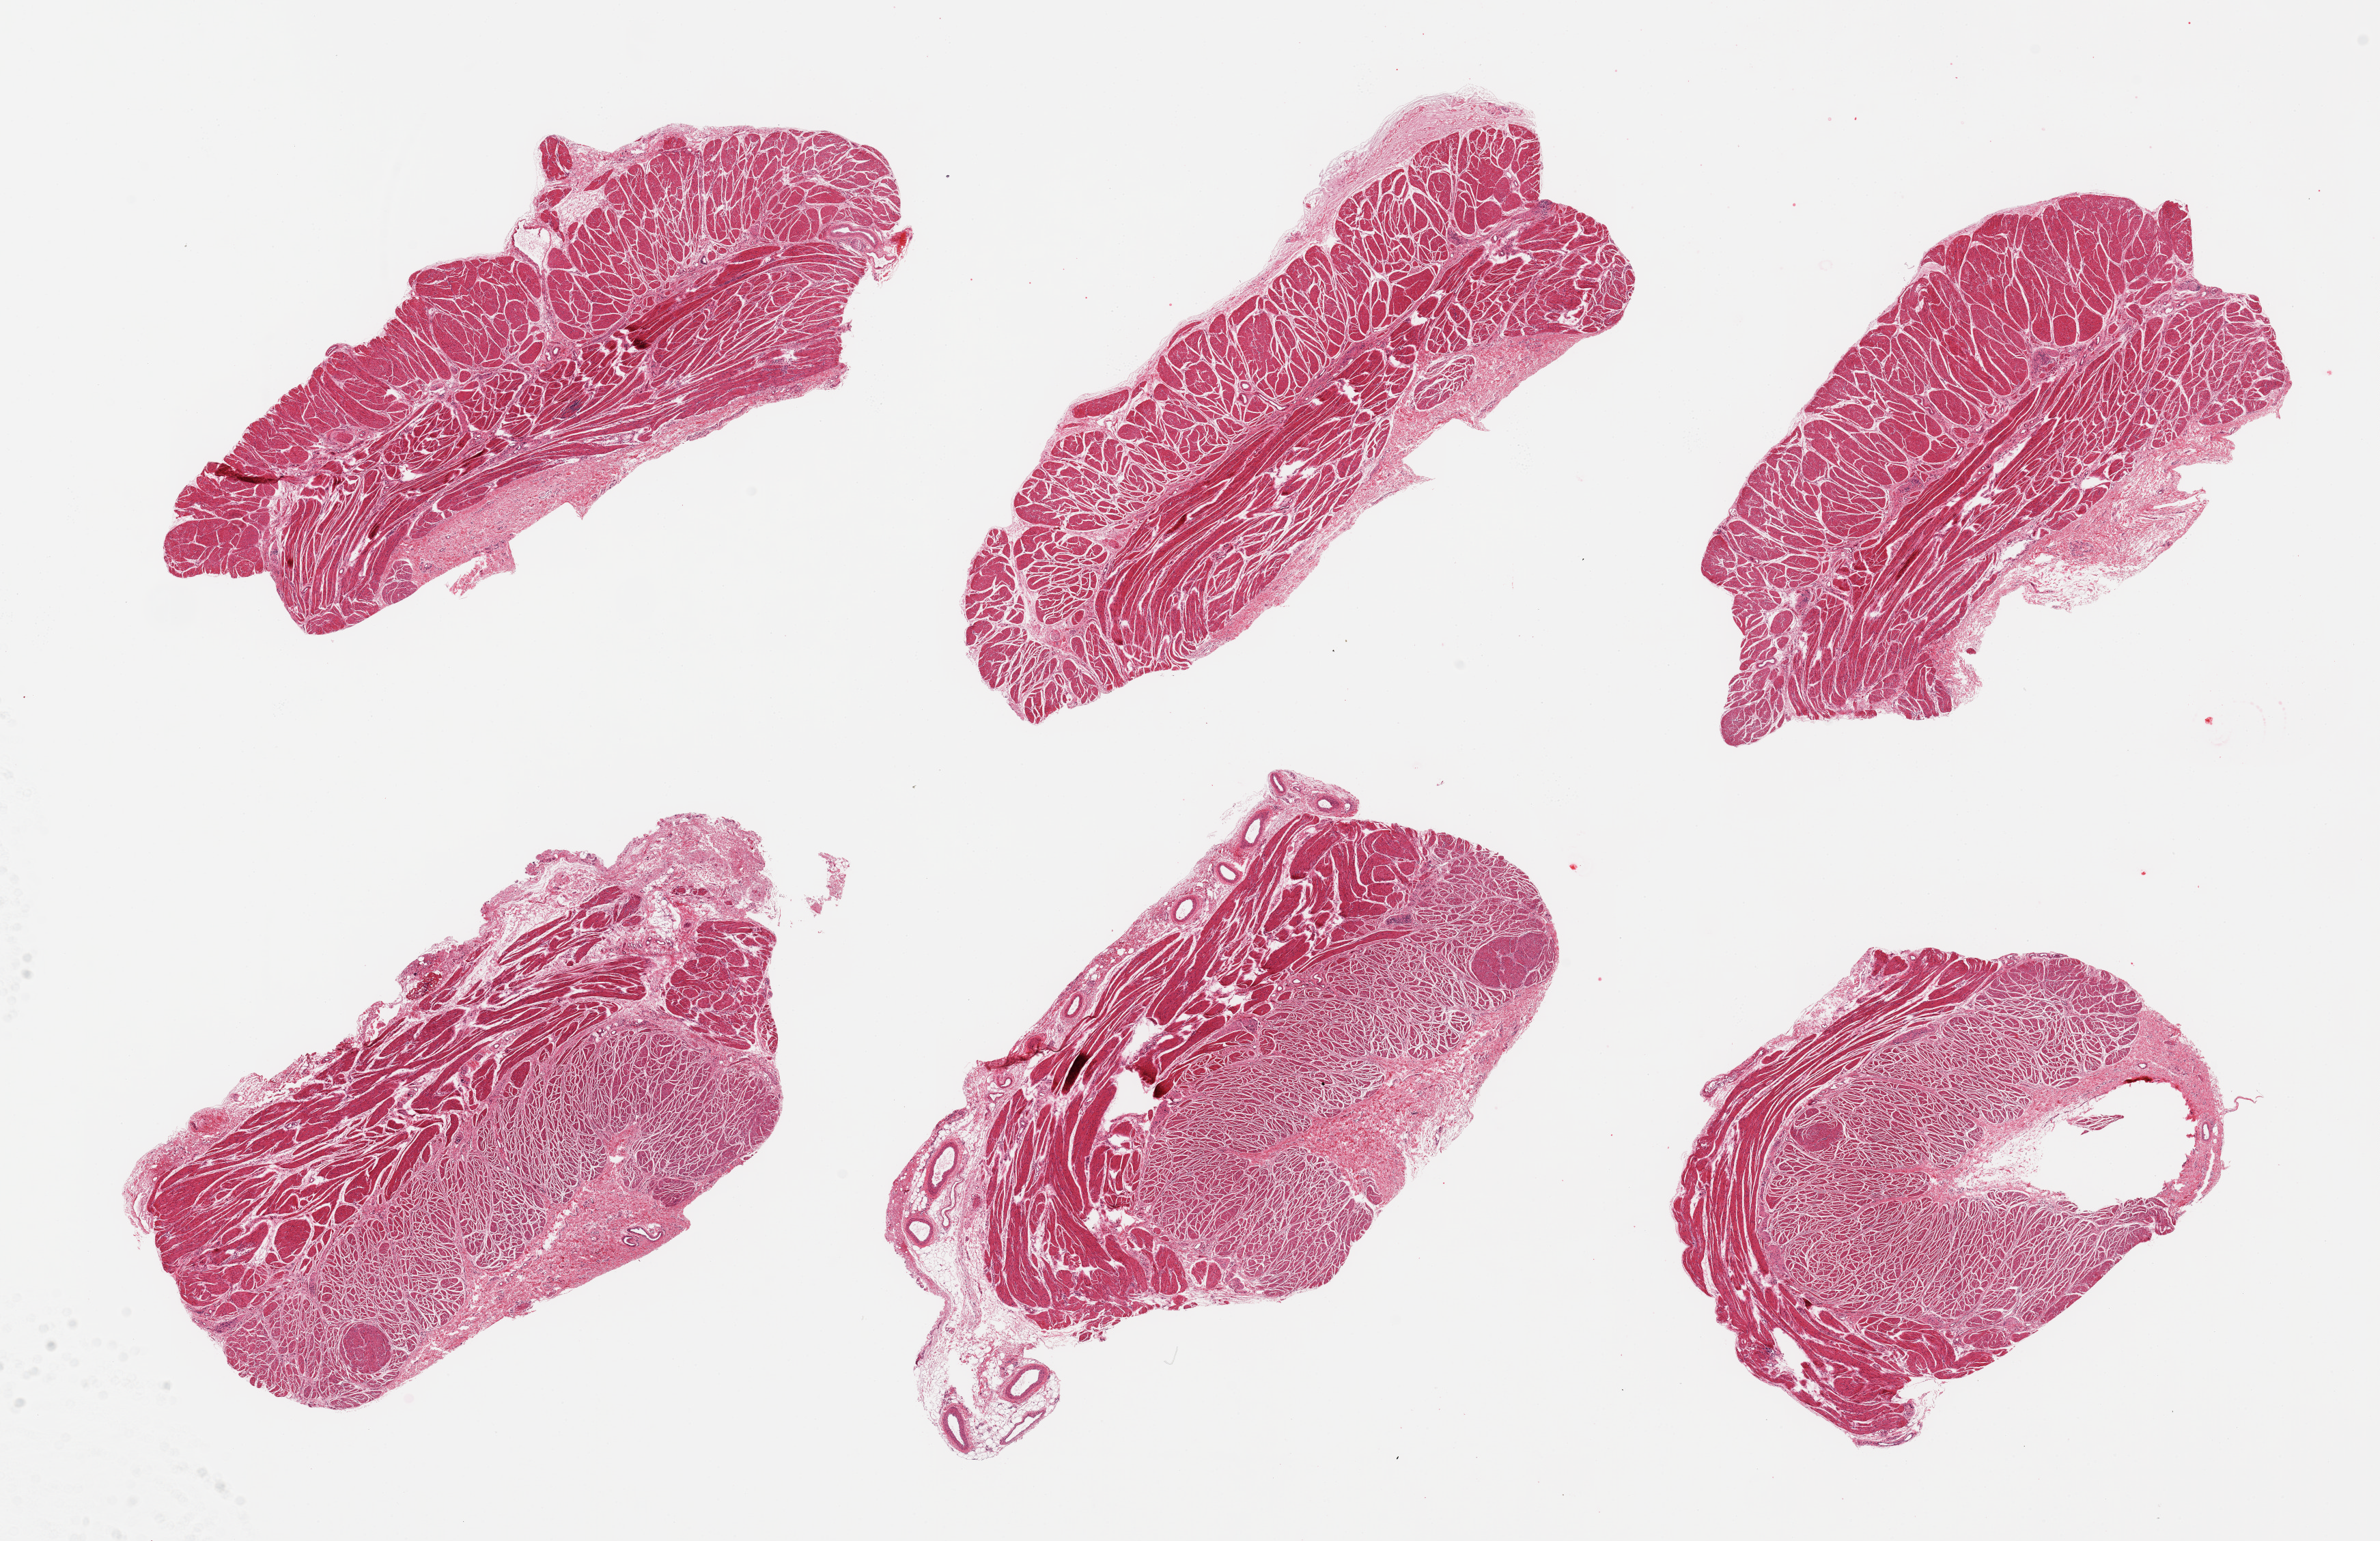
Digitized H&E-stained section, brightfield, whole scanned area (about 27.6 x 17.9 mm) shown as a low-resolution overview; PAXgene-fixed paraffin-embedded (PFPE) section; target tissue: esophageal muscle; tissue donor sample.
Reviewer comment on this tissue sample: 6 pieces, all muscularis, trace serosa.